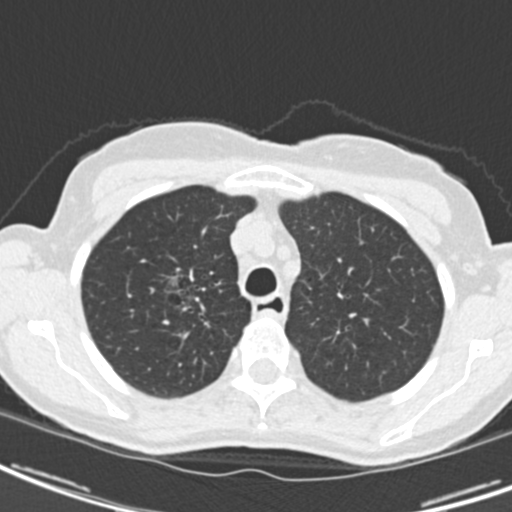
Low-dose screening chest CT, one axial slice. Reconstruction kernel B30f. Lung window (W 1500 / L -600 HU). 2 mm slice thickness. 512 × 512 image matrix.
Annotated regions visible in this slice (manually delineated by an expert):
- lesion 1 (tumor, upper lobe of right lung): bounding box [x1, y1, x2, y2] px = [164, 274, 199, 305]